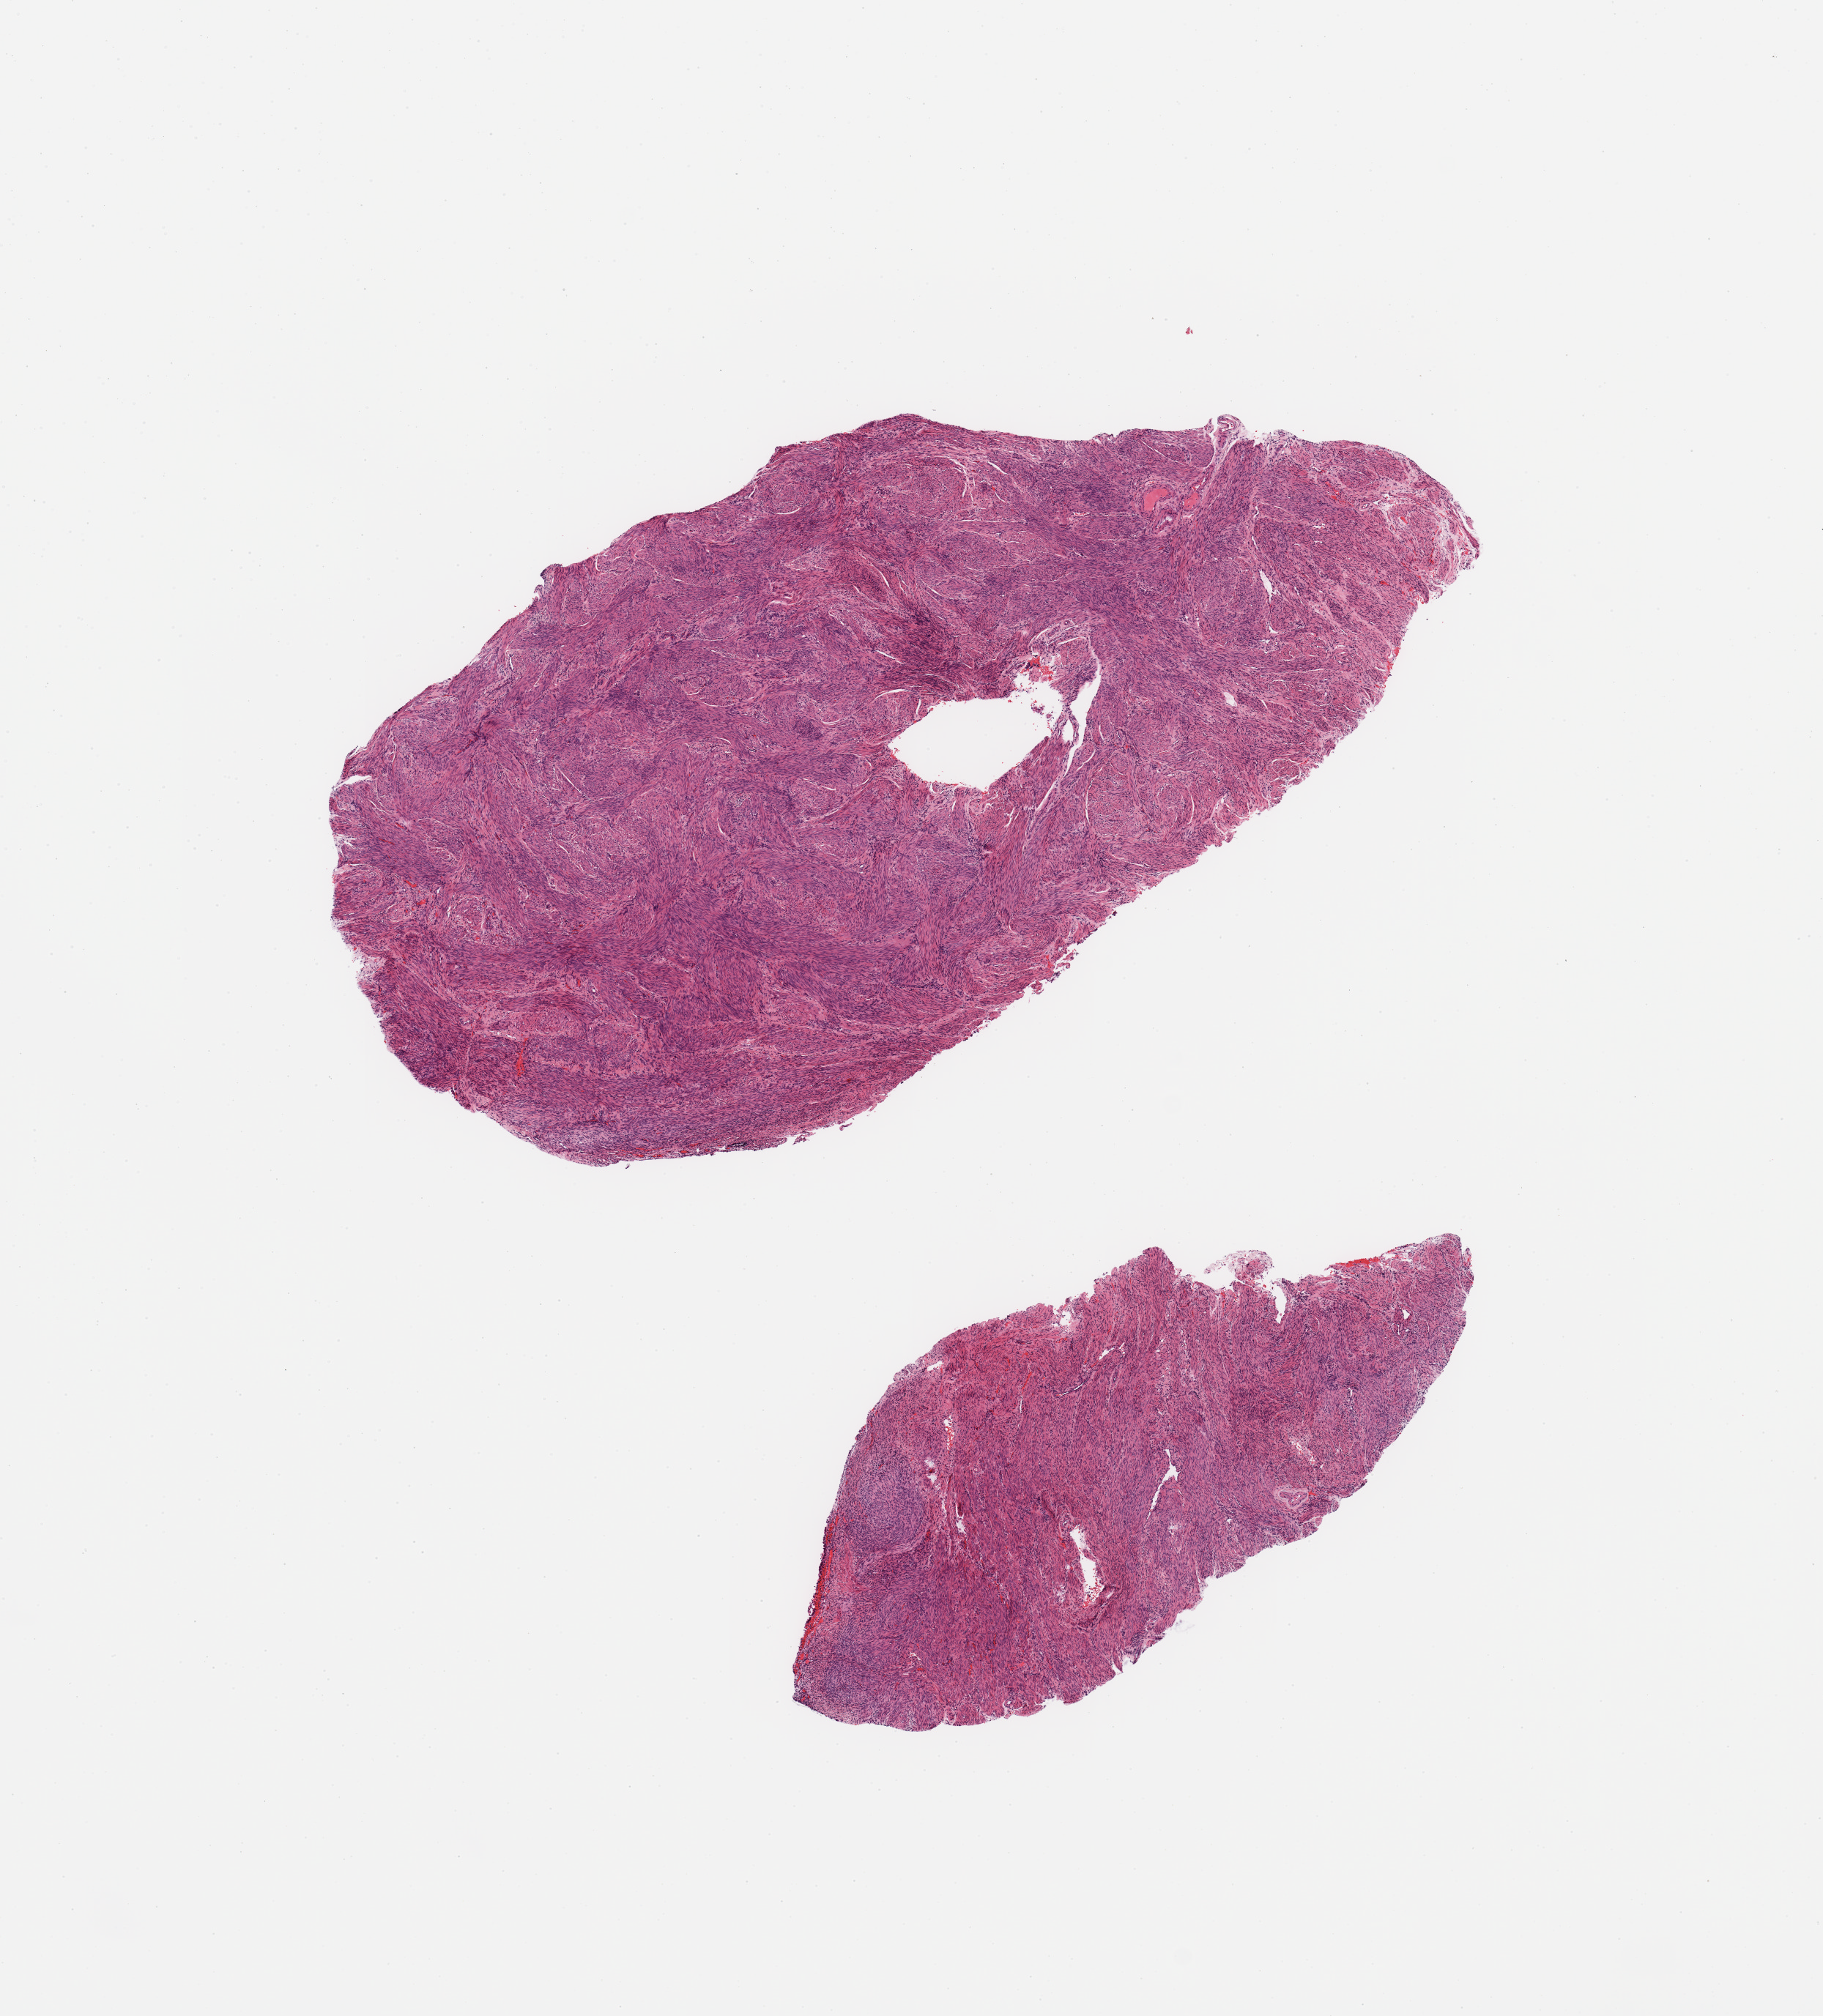
Digitized H&E-stained tissue section (whole slide), a low-resolution overview of the entire scanned area, about 9.8 x 10.9 mm. Normal (non-tumour) tissue sample, uterus. 73-year-old female patient.
* this section: normal (non-tumour) tissue from the same patient
* patient diagnosis: Endometrioid adenocarcinoma, NOS